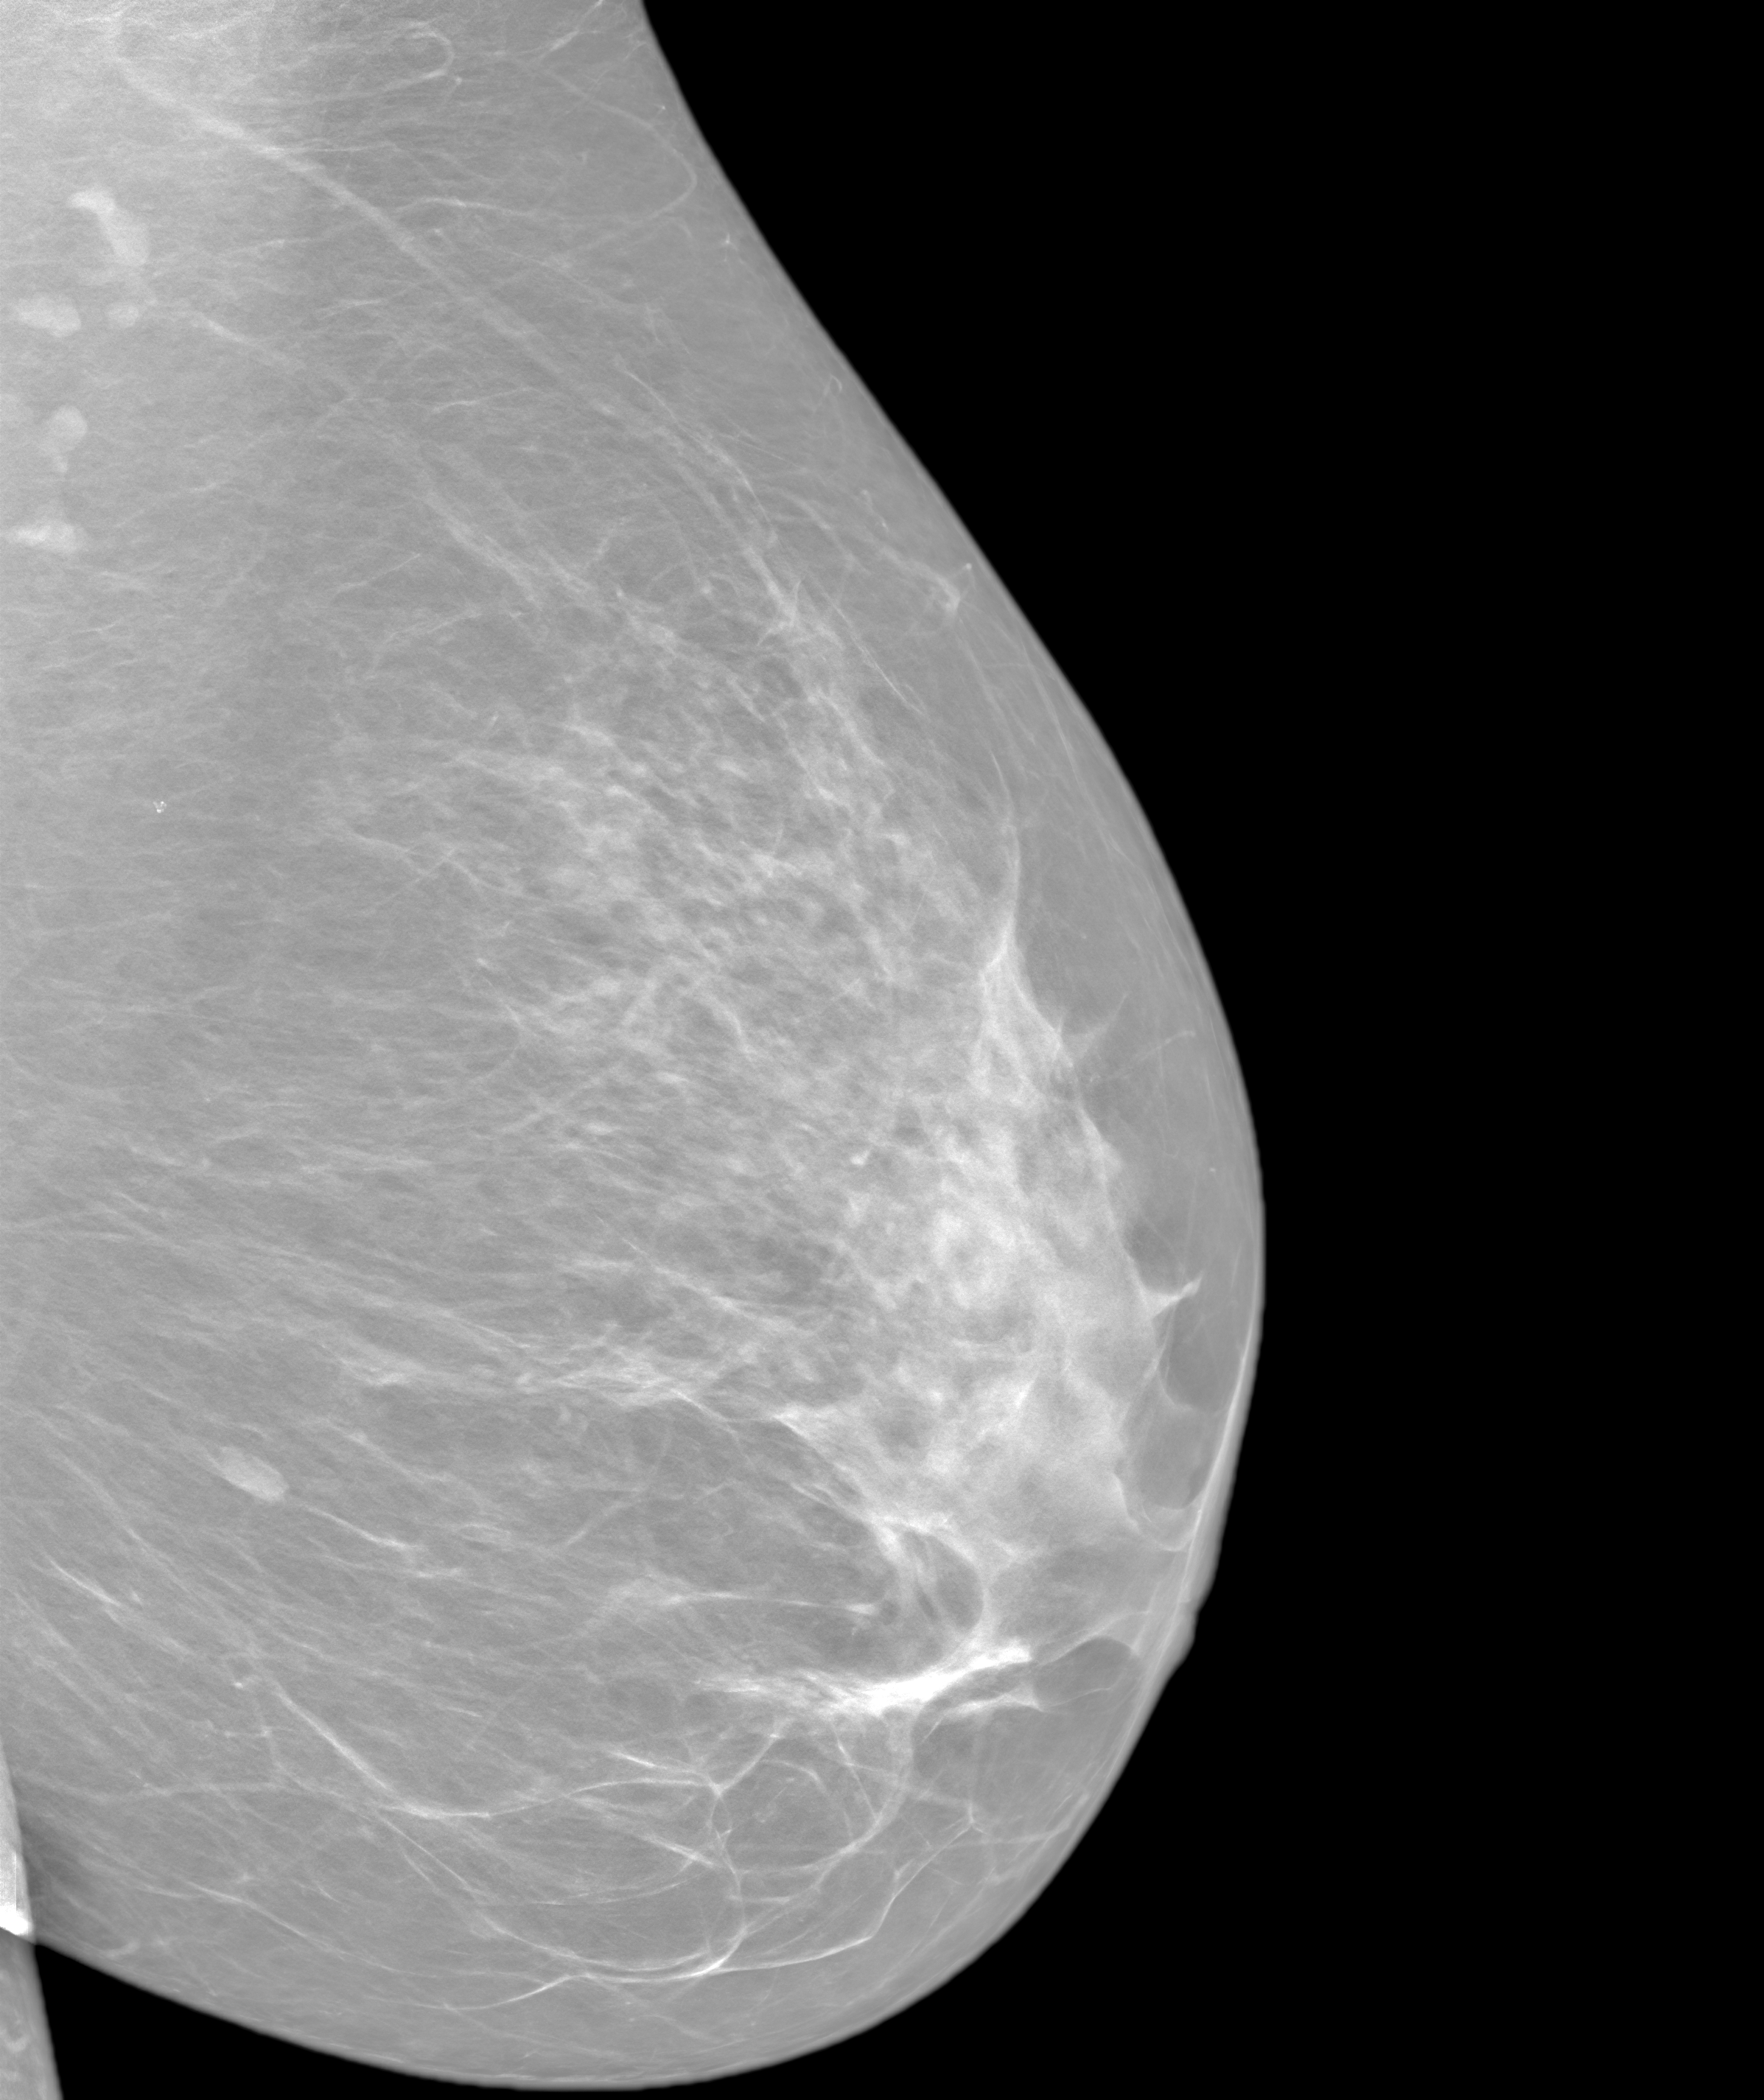
Screening examination. Patient aged 57 years (female).
Image type: synthesized 2-D view from tomosynthesis. Breast: left. Projection: MLO view.